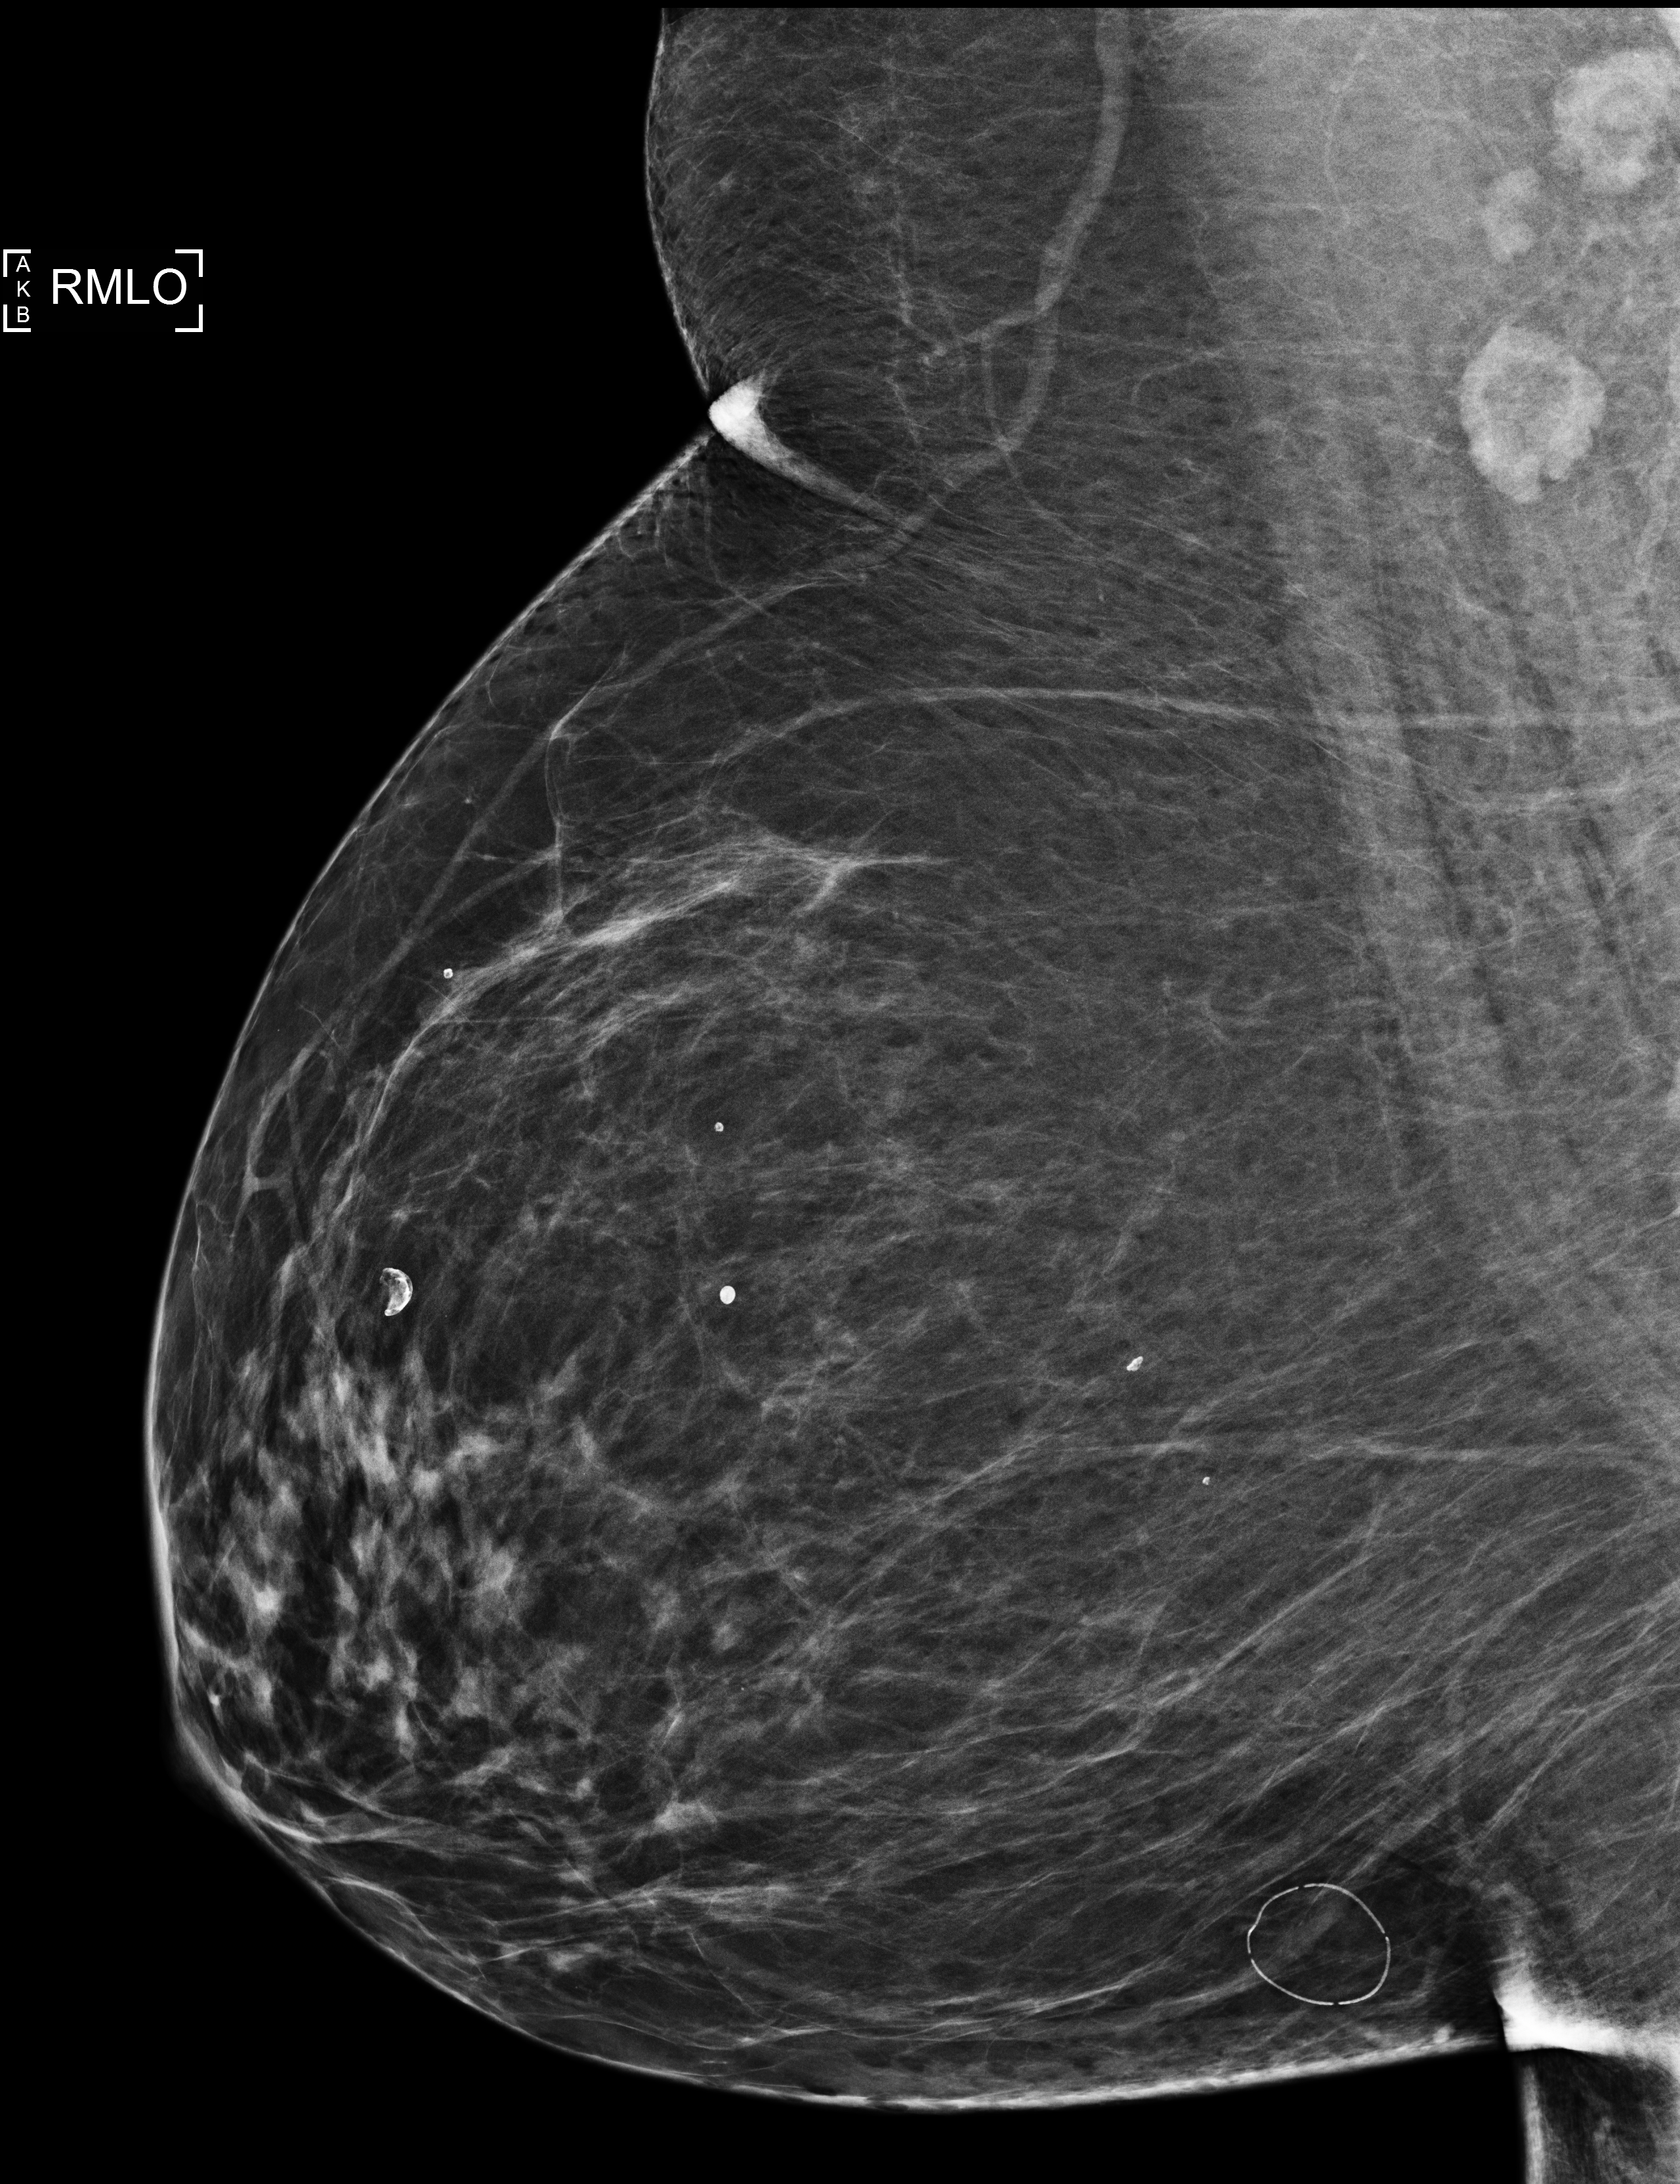
Full-field digital mammogram (FFDM), right breast, medio-lateral oblique projection, screening examination, compressed breast thickness 69 mm. Female patient, age 66 years.
Breast density at the screening exam (both breasts): scattered fibroglandular densities (BI-RADS density category b). Final BI-RADS category for the screening round (tomosynthesis exam, both breasts): category 1. Recall: no recall after this screen.